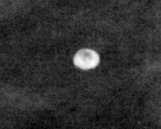
Crop from a digitized film mammogram around one marked abnormality, right breast, CC view.
Calcifications, distribution regional; BI-RADS assessment category 2; subtlety rating 3 on a 1 (subtle) to 5 (obvious) scale; benign without callback (not worked up further).